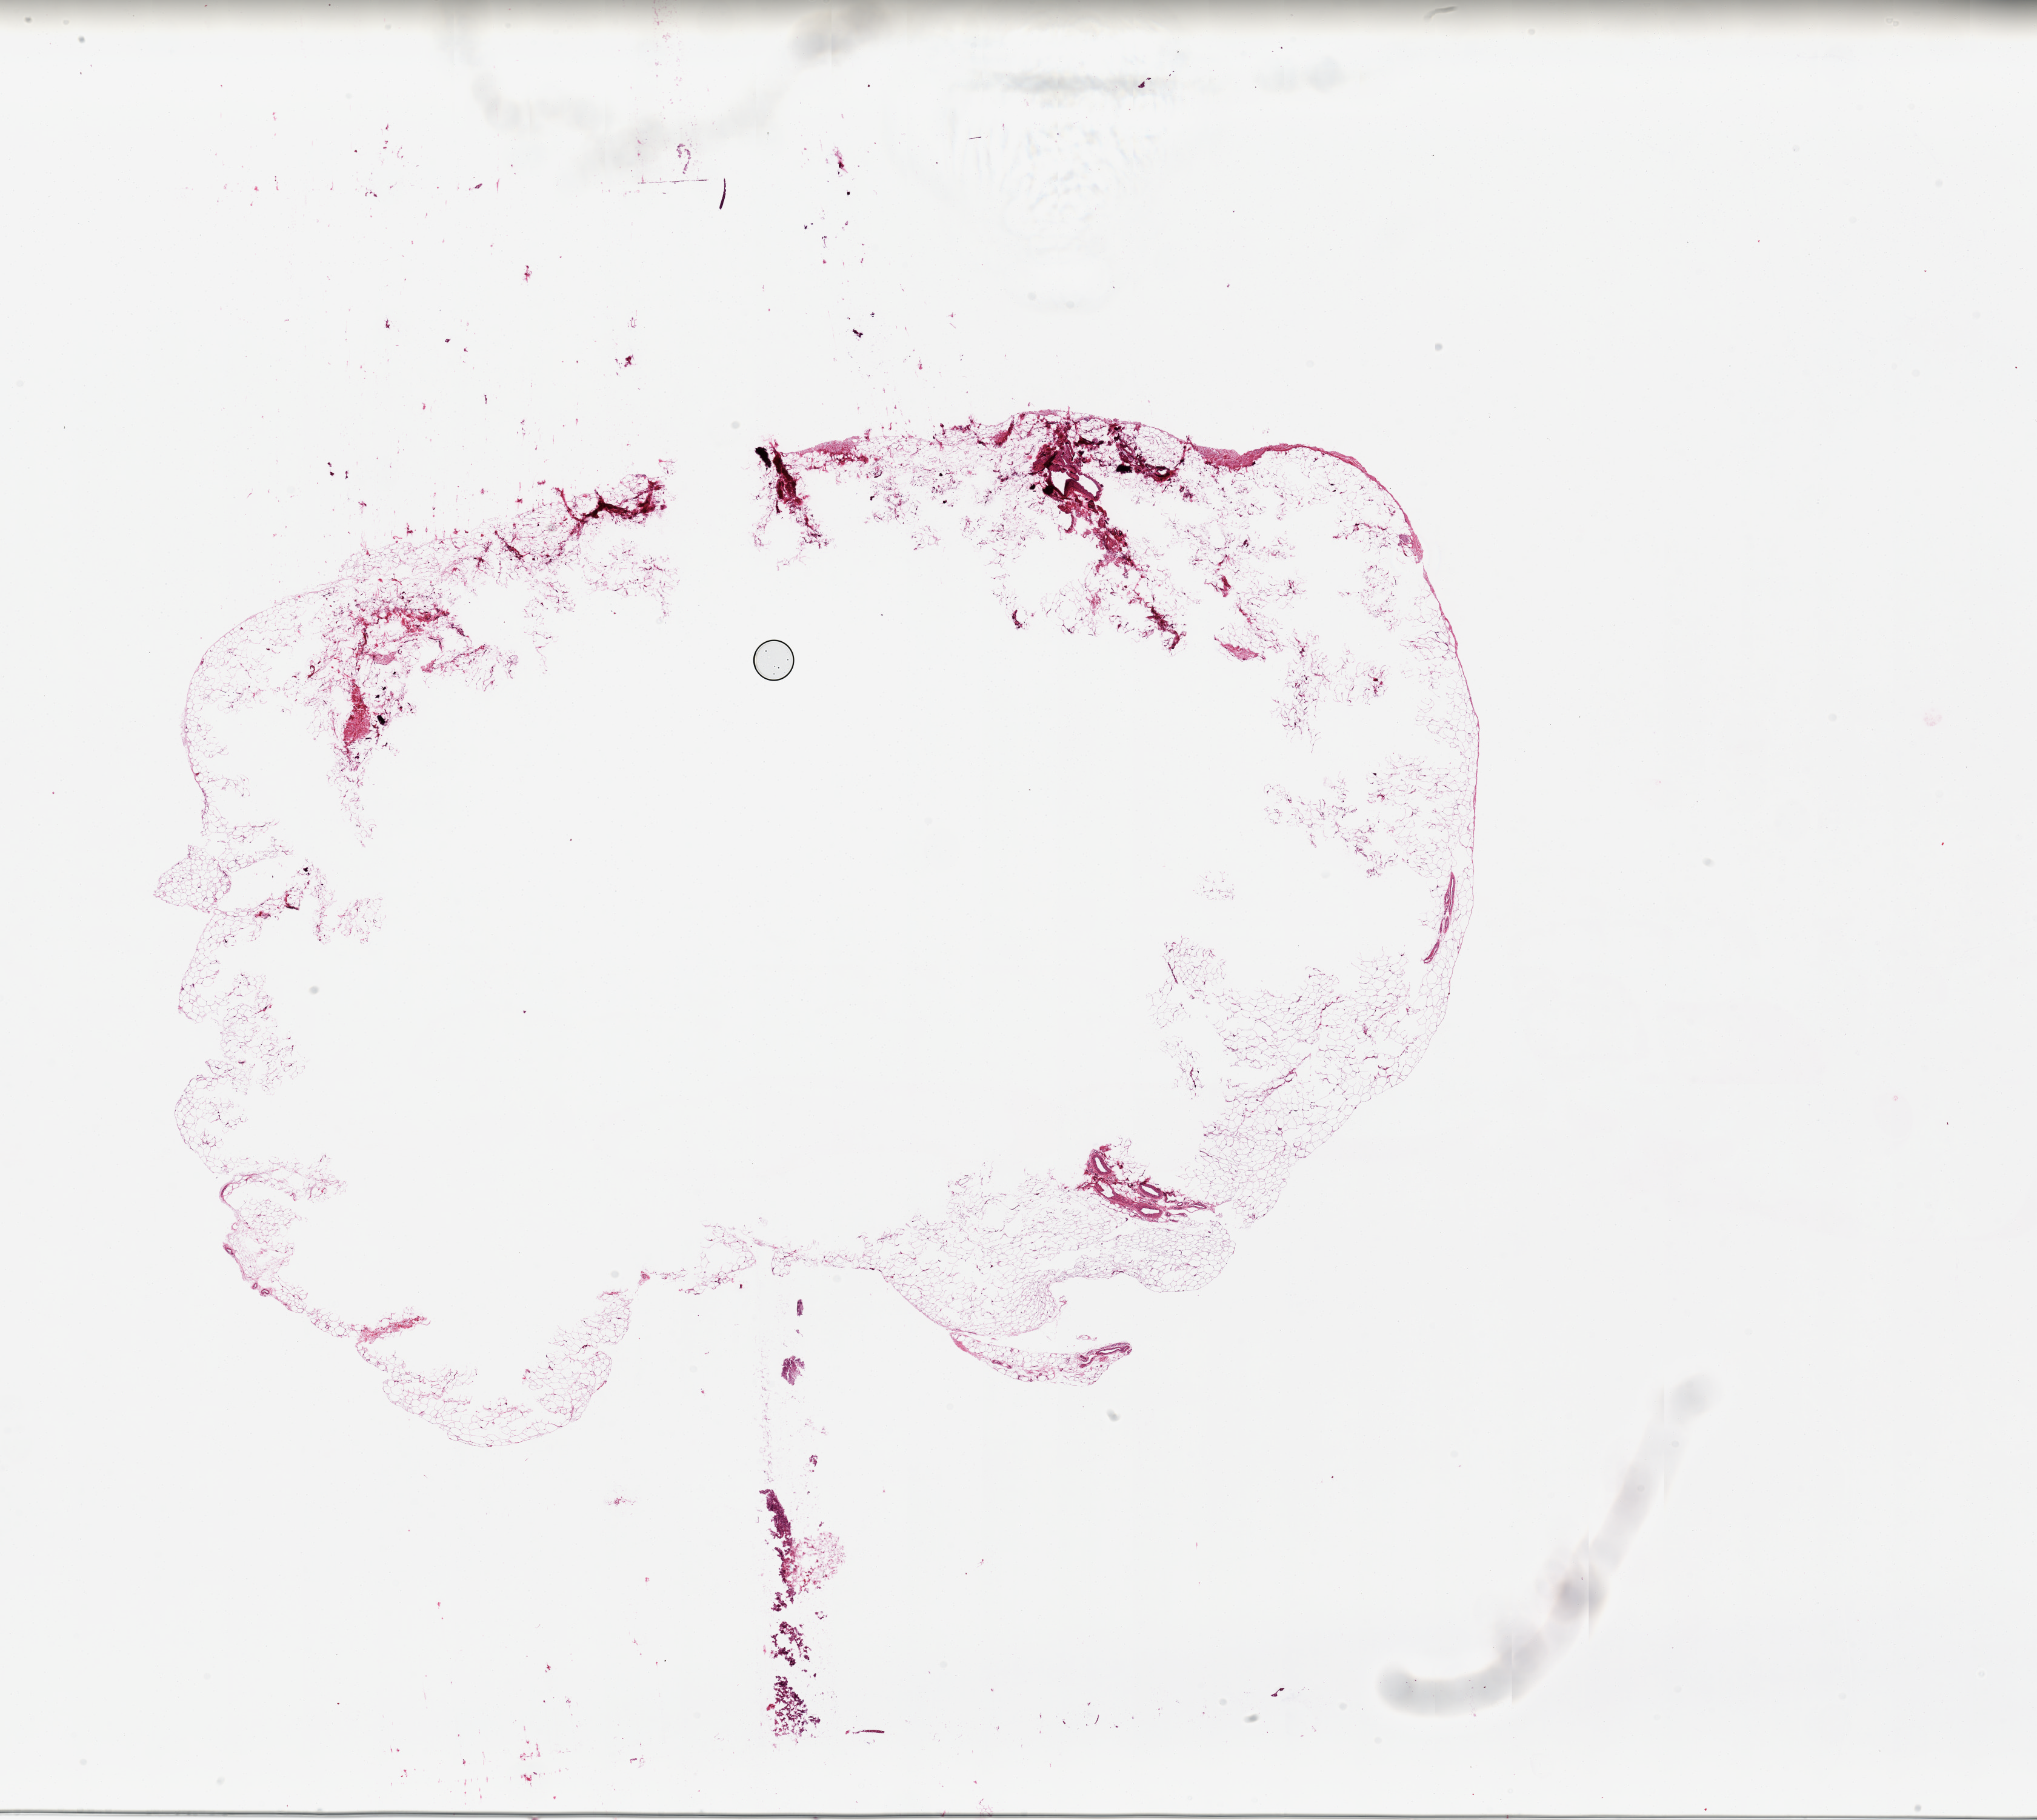
H&E whole-slide image — low-resolution overview of the scanned area, about 26.6 x 23.7 mm. PAXgene-fixed, paraffin-embedded tissue. Section of adipose tissue (target tissue). Tissue donor sample. Donor: male.
* pathologist's review note for this sample: Oversized (17mm) aliquot with central portion unfixed. Thin outer rim preserved